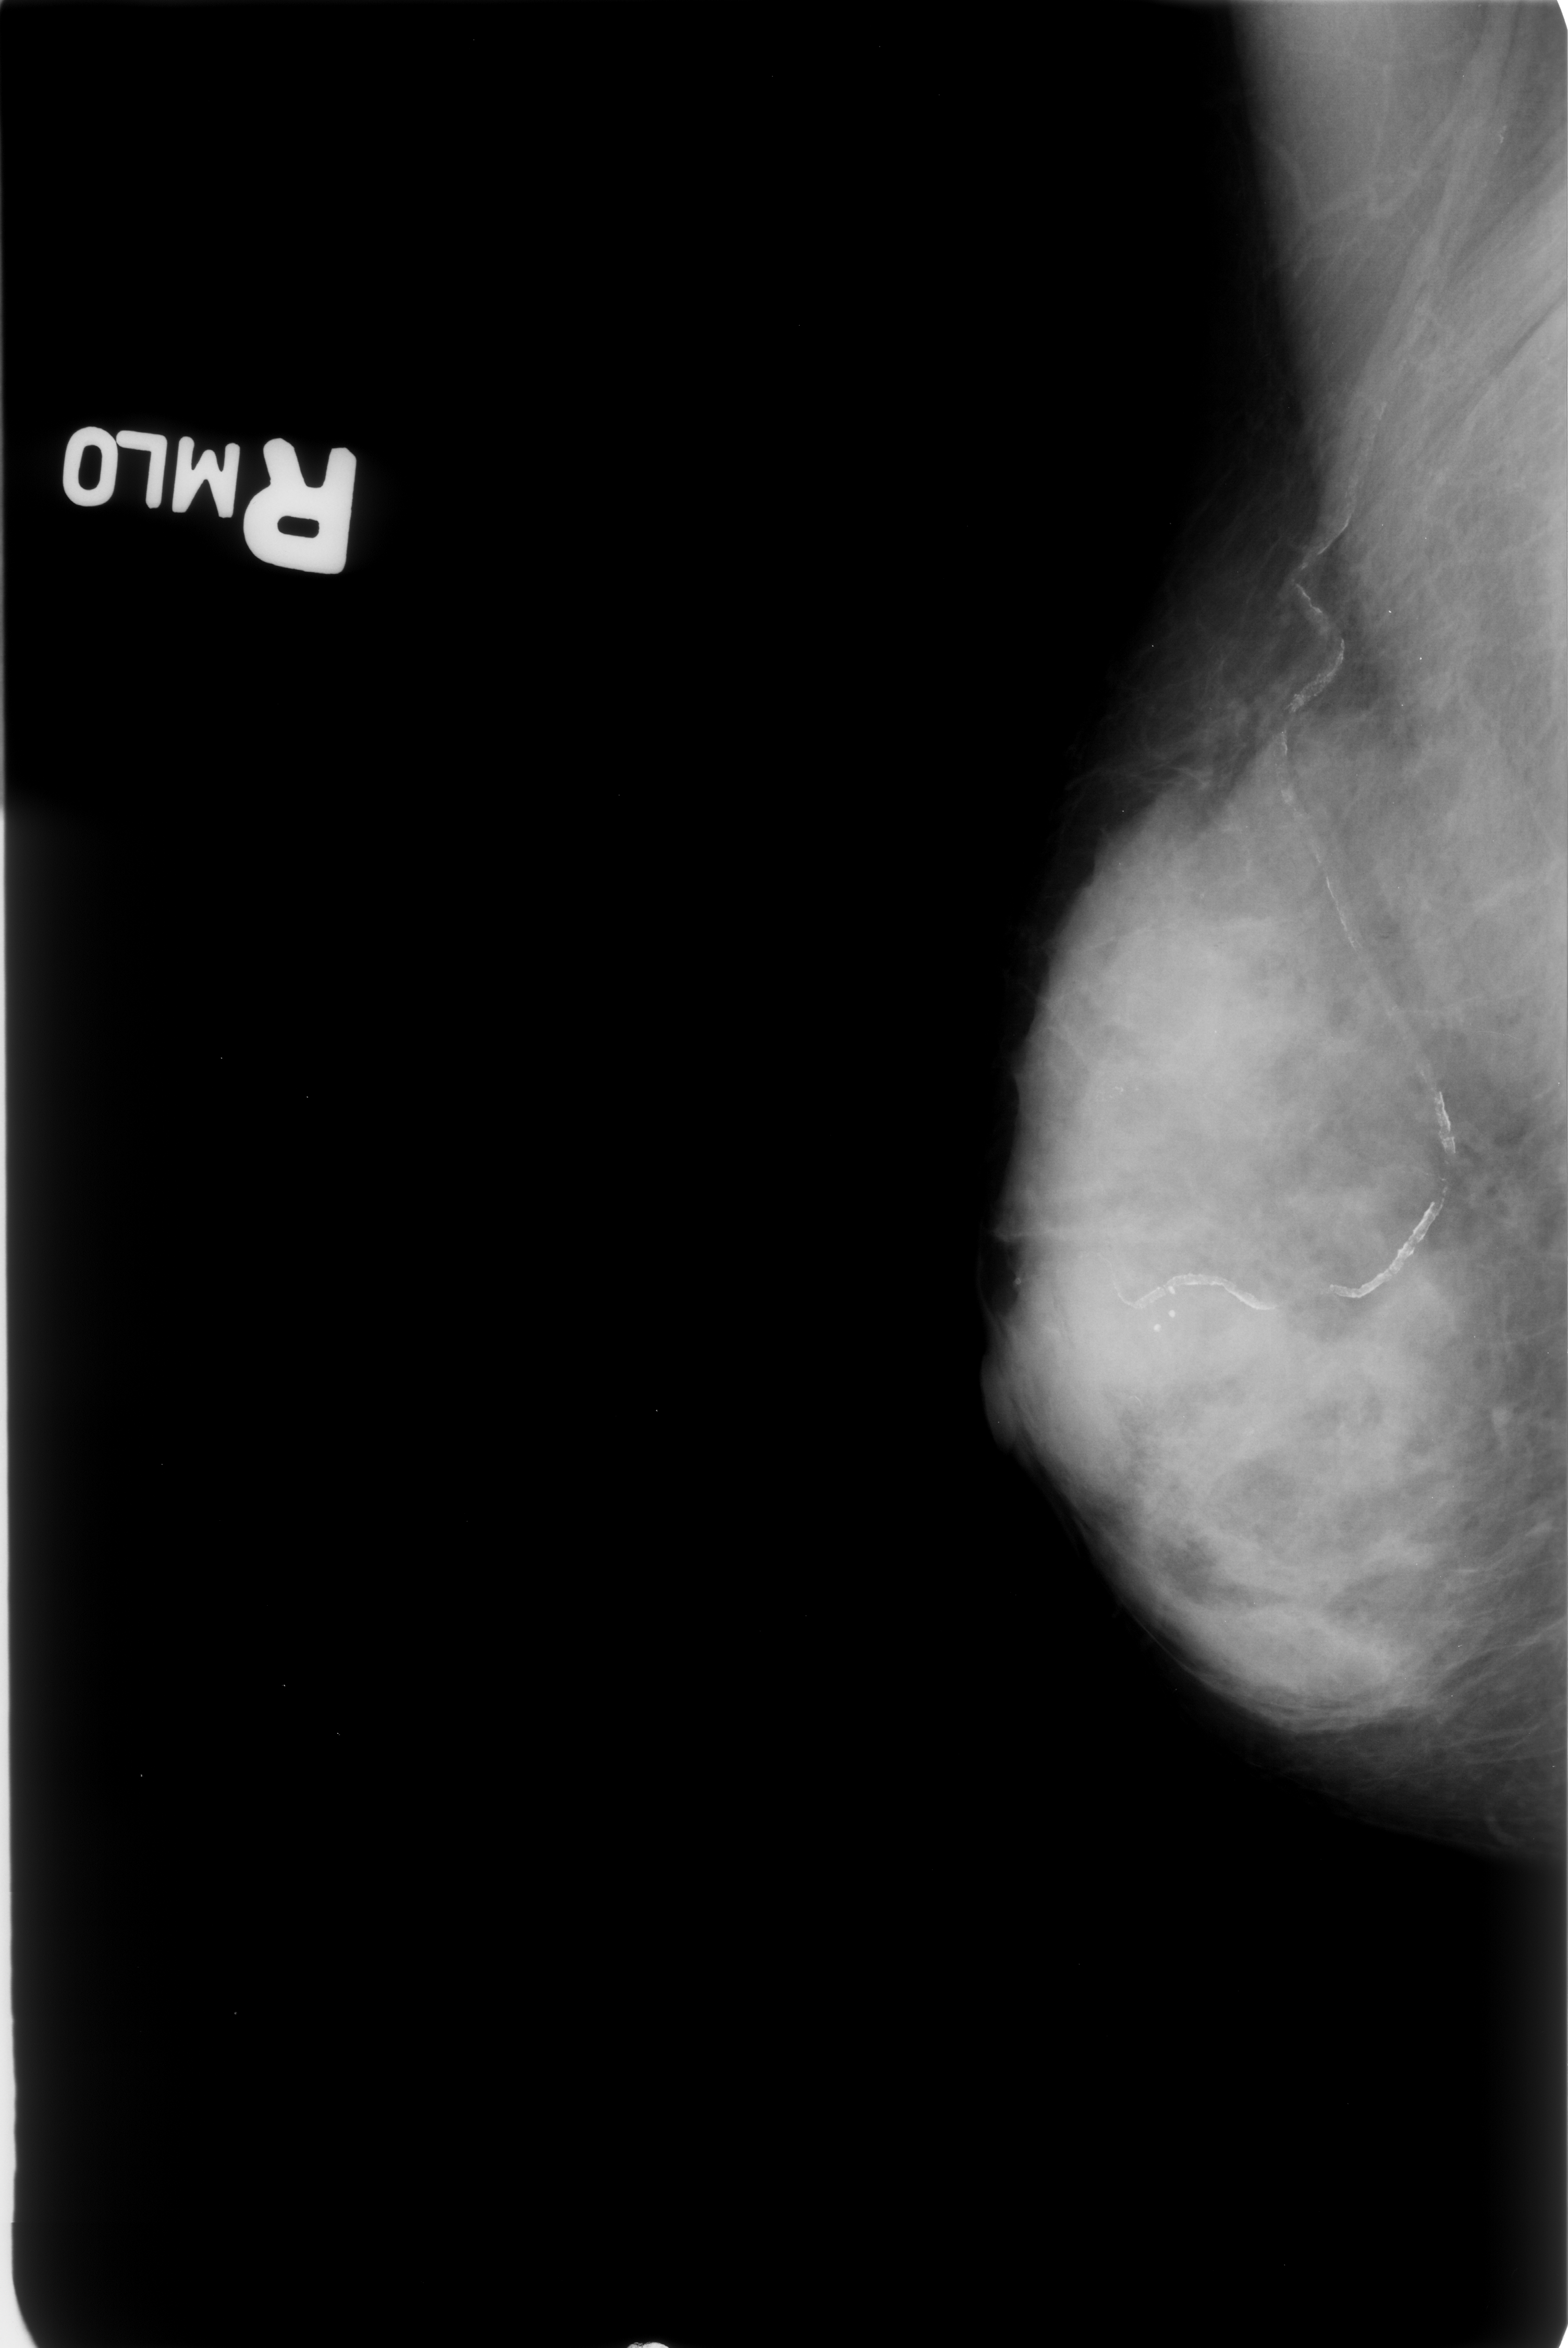
Digitized screen-film mammogram, right breast, MLO view, breast composition: extremely dense (BI-RADS density category 4 of 4).
- Radiologist-marked abnormalities on this image: calcifications, morphology pleomorphic, distribution clustered; BI-RADS assessment category 4; pathology result (as recorded, not read from the image): benign.